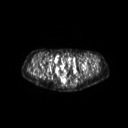
FDG PET of an extremity soft-tissue mass (from a PET/CT study), one axial slice. 3.27 mm slice thickness. 128 × 128 image matrix, field of view 600 × 600 mm. Female patient, age 57 years. Case-level facts recorded for this patient, not image findings: histological type: epithelioid sarcoma with vascular differentiation; site of the primary tumour: right buttock.
Annotated regions visible in this slice (expert contour drawn on MRI and transferred to this co-registered scan by the dataset authors):
- gross tumour volume (mass): bounding box [x1, y1, x2, y2] px = [28, 69, 36, 72]